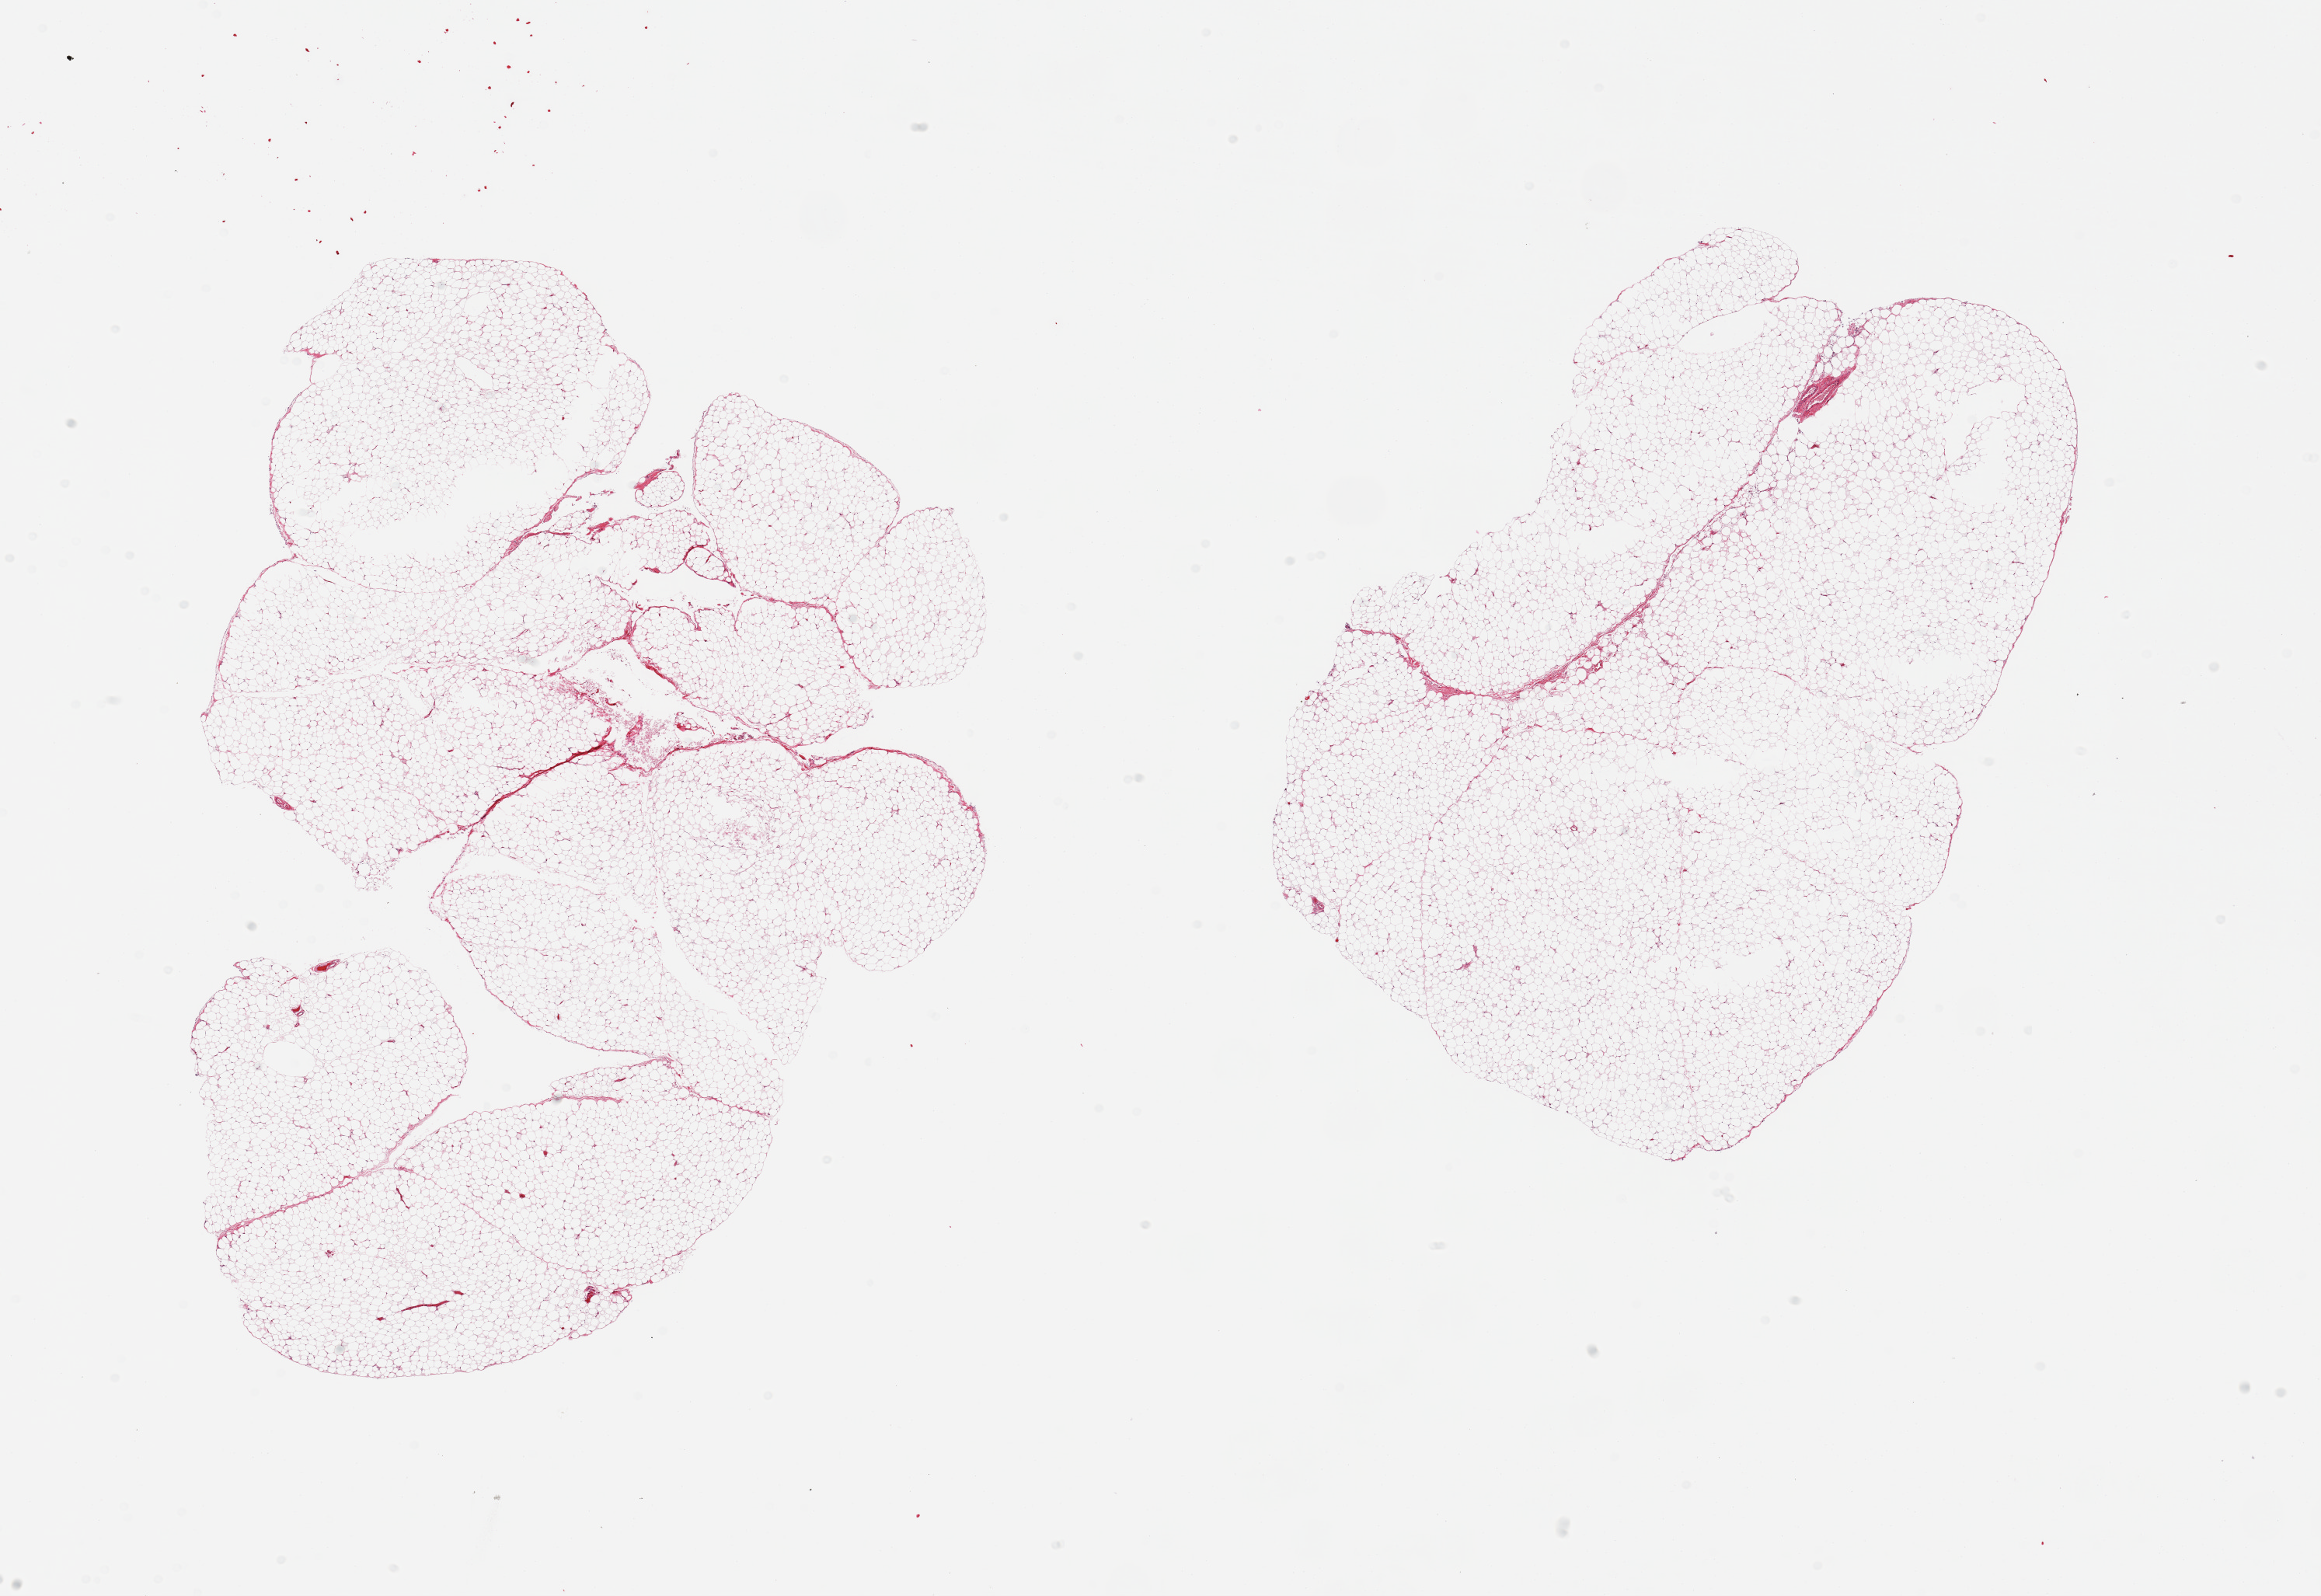
Digitized haematoxylin and eosin-stained section — shown as a low-resolution overview of the whole scanned area (about 23.6 x 16.2 mm); PAXgene-fixed paraffin-embedded (PFPE) section; target tissue: omentum; tissue donor sample. Donor sex: male.
Reviewer comment on this tissue sample: 2 pieces; minimal fibrous content.